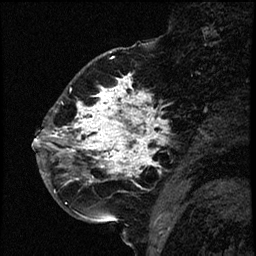
Breast MRI (dynamic contrast-enhanced), one sagittal slice. Slice 25 of 66 in the series (ordered by position). Dynamic contrast-enhanced study with each time point stored as its own series, time point 2 of 3 at this slice position (early post-contrast, ordered by acquisition time). 1.5 T. TE 4.2 ms, TR 17.6 ms. 2 mm slice thickness. 256 × 256 image matrix, field of view 200 × 200 mm. Female patient. From the clinical record (not read from this slice): setting: breast cancer imaged before/during neoadjuvant chemotherapy; receptor status: HER2-positive.
Outlined on this slice (semi-automatic segmentation, software-assisted and operator-edited):
- analysis volume of interest (the breast-tissue region the enhancement analysis was run in; not a lesion): bounding box (x1, y1, x2, y2) in pixels: (52, 69, 177, 209)
- tumour enhancement mask (voxels above the 100 % enhancement threshold inside the analysis volume of interest): (52, 75, 164, 184)